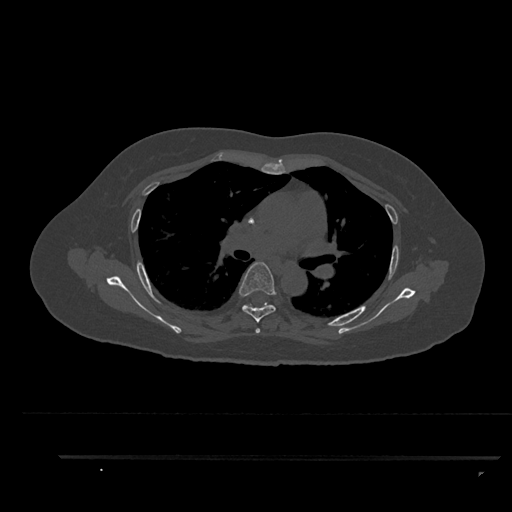
CT including the spine, one axial slice; slice 597 of 797 in the series (ordered by position); 120 kVp; bone window (W 1800 / L 400 HU); 512 × 512 image matrix. Patient: female, 44 years. Case-level facts recorded for this patient, not image findings: primary cancer: renal; vertebrae with lytic lesions (as recorded): L1.
Structures marked on this image (semi-automatically segmented with operator editing):
- T4 vertebra: bounding box <255,328,260,333> (left, top, right, bottom; pixels)
- T5 vertebra: <239,262,276,323>
- T6 vertebra: <242,302,269,307>